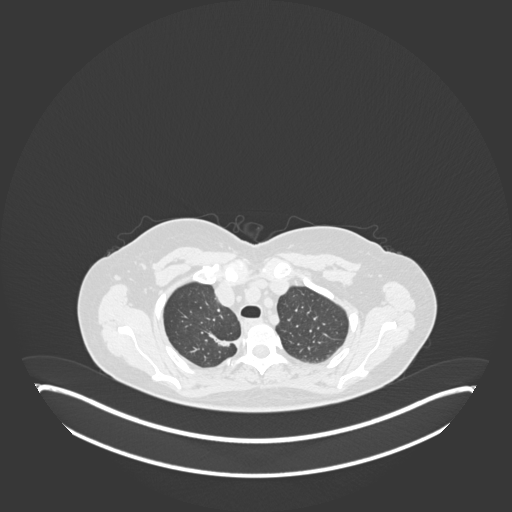
Chest CT, one axial slice. Position 147 of 181 along the scan axis. Lung window (W 1500 / L -600 HU). 512 × 512 image matrix. Female patient, age 65 years. From the clinical record (not read from this slice): clinical TNM (as recorded): T1b N0 M0.
Outlined on this slice (rectangle marked by the reading radiologist):
- lung tumour (recorded histology: adenocarcinoma): bounding box (x1, y1, x2, y2) in pixels: (202, 328, 244, 353)